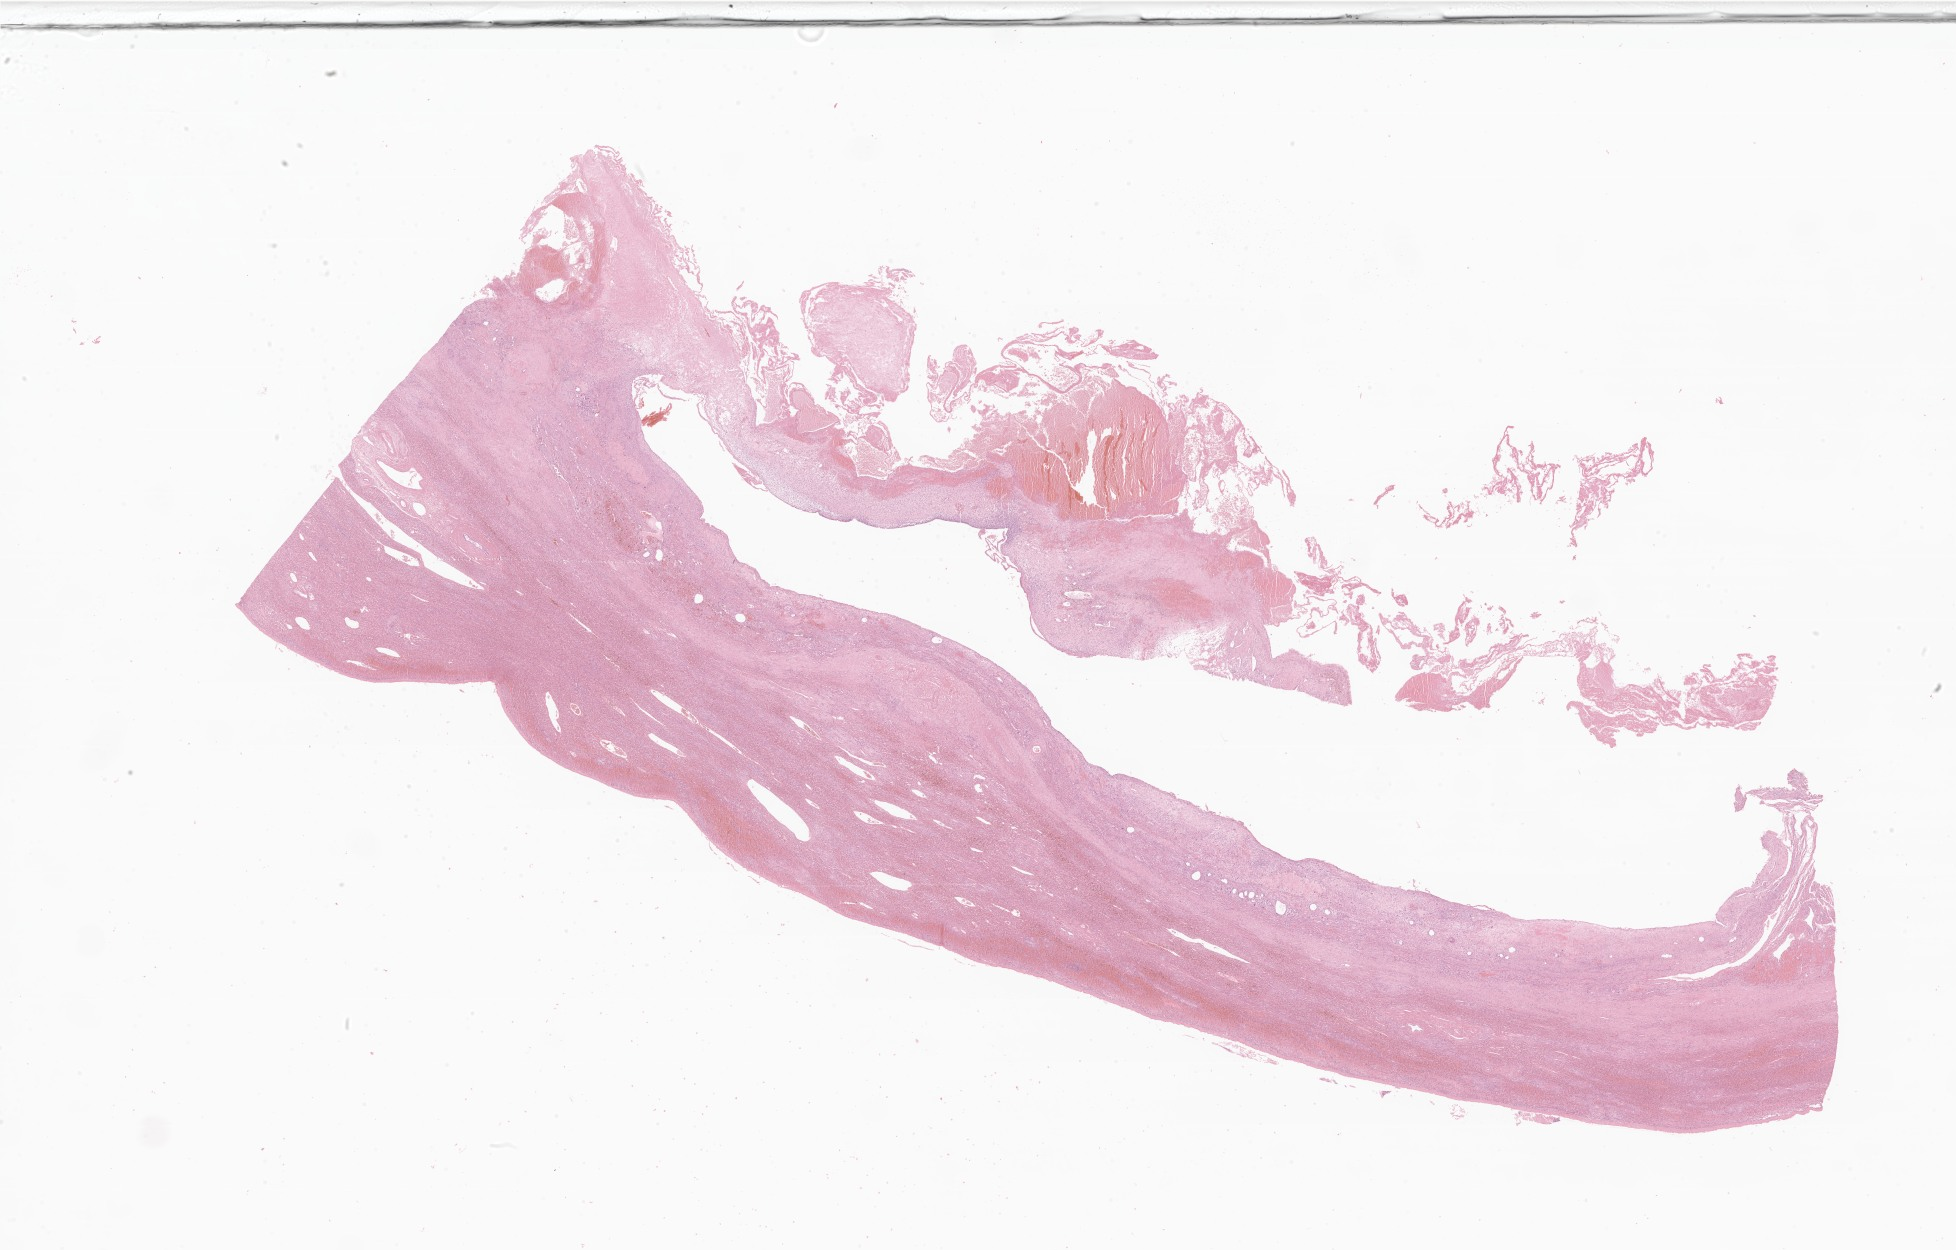
Digitized hematoxylin and eosin (H&E)-stained section of tumor tissue from the liver — a low-resolution overview of the entire scanned area, about 33.0 x 21.1 mm, FFPE section. Female patient, age 143 months.
Diagnosis (ICD-O-3 morphology term): Embryonal sarcoma.